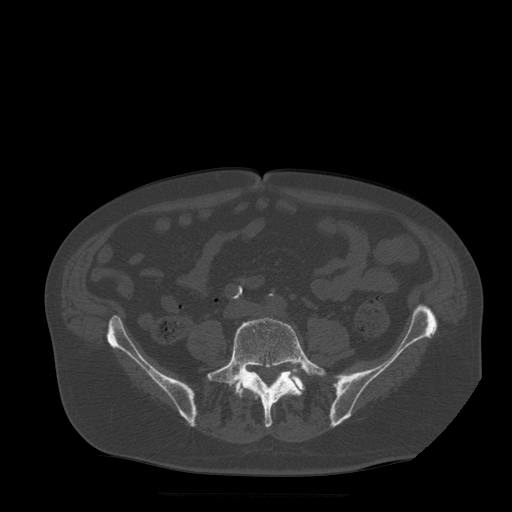
CT including the spine, one axial slice. Slice 89 of 522 in the series (ordered by position). Bone window (W 1800 / L 400 HU). 1.25 mm slice thickness. 512 × 512 image matrix, field of view 420 × 420 mm. Patient age 72 years. Case-level facts recorded for this patient, not image findings: primary cancer: prostate.
Outlined on this slice (semi-automatic segmentation, software-assisted and operator-edited):
- L5 vertebra: box from (x=207, y=318) to (x=327, y=428) px